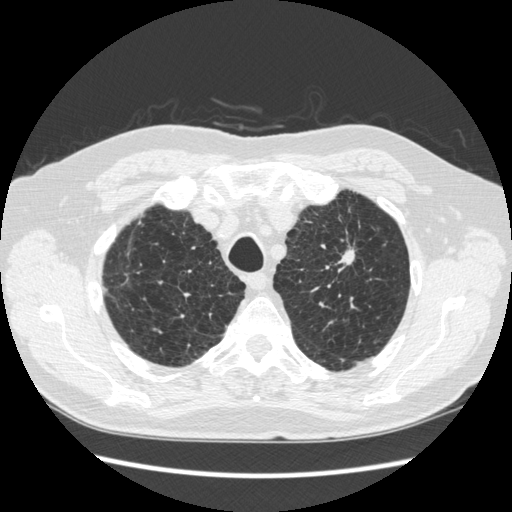
Axial slice from a low-dose chest CT screening exam; third annual screen; lung window (W 1500 / L -600 HU); 1.25 mm slice thickness; 120 kVp; slice 47 of 267 in the series. Male, age 70 years at enrolment.
Expert-annotated lung lesion, bounding box <323,216,373,281> (left, top, right, bottom; pixels). The screening reader recorded 2 non-calcified nodules or masses ≥4 mm on this exam (left upper lobe, right lower lobe); which of them this box marks is not recorded. Lung cancer was diagnosed 92 days after this screen: squamous cell carcinoma, NOS, left upper lobe, moderately differentiated (G2), stage IA (AJCC 6th edition), 18 mm at pathology.